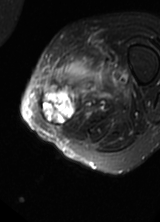
MRI of an extremity soft-tissue mass, one axial slice. Position 17 of 69 along the scan axis. T2-weighted fat-saturated. MR volume resampled by the dataset authors to the PET/CT grid (not the native acquisition matrix). 3.27 mm slice thickness. 160 × 222 image matrix, field of view 156 × 217 mm. Female patient. From the clinical record (not read from this slice): histological type: pleomorphic leiomyosarcoma; grade: high; site of the primary tumour: left thigh.
Outlined on this slice (expert contour drawn on MRI and transferred to this co-registered scan by the dataset authors):
- gross tumour volume including surrounding oedema: bounding box [x1, y1, x2, y2] px = [39, 54, 126, 128]
- gross tumour volume (mass): [41, 86, 76, 126]